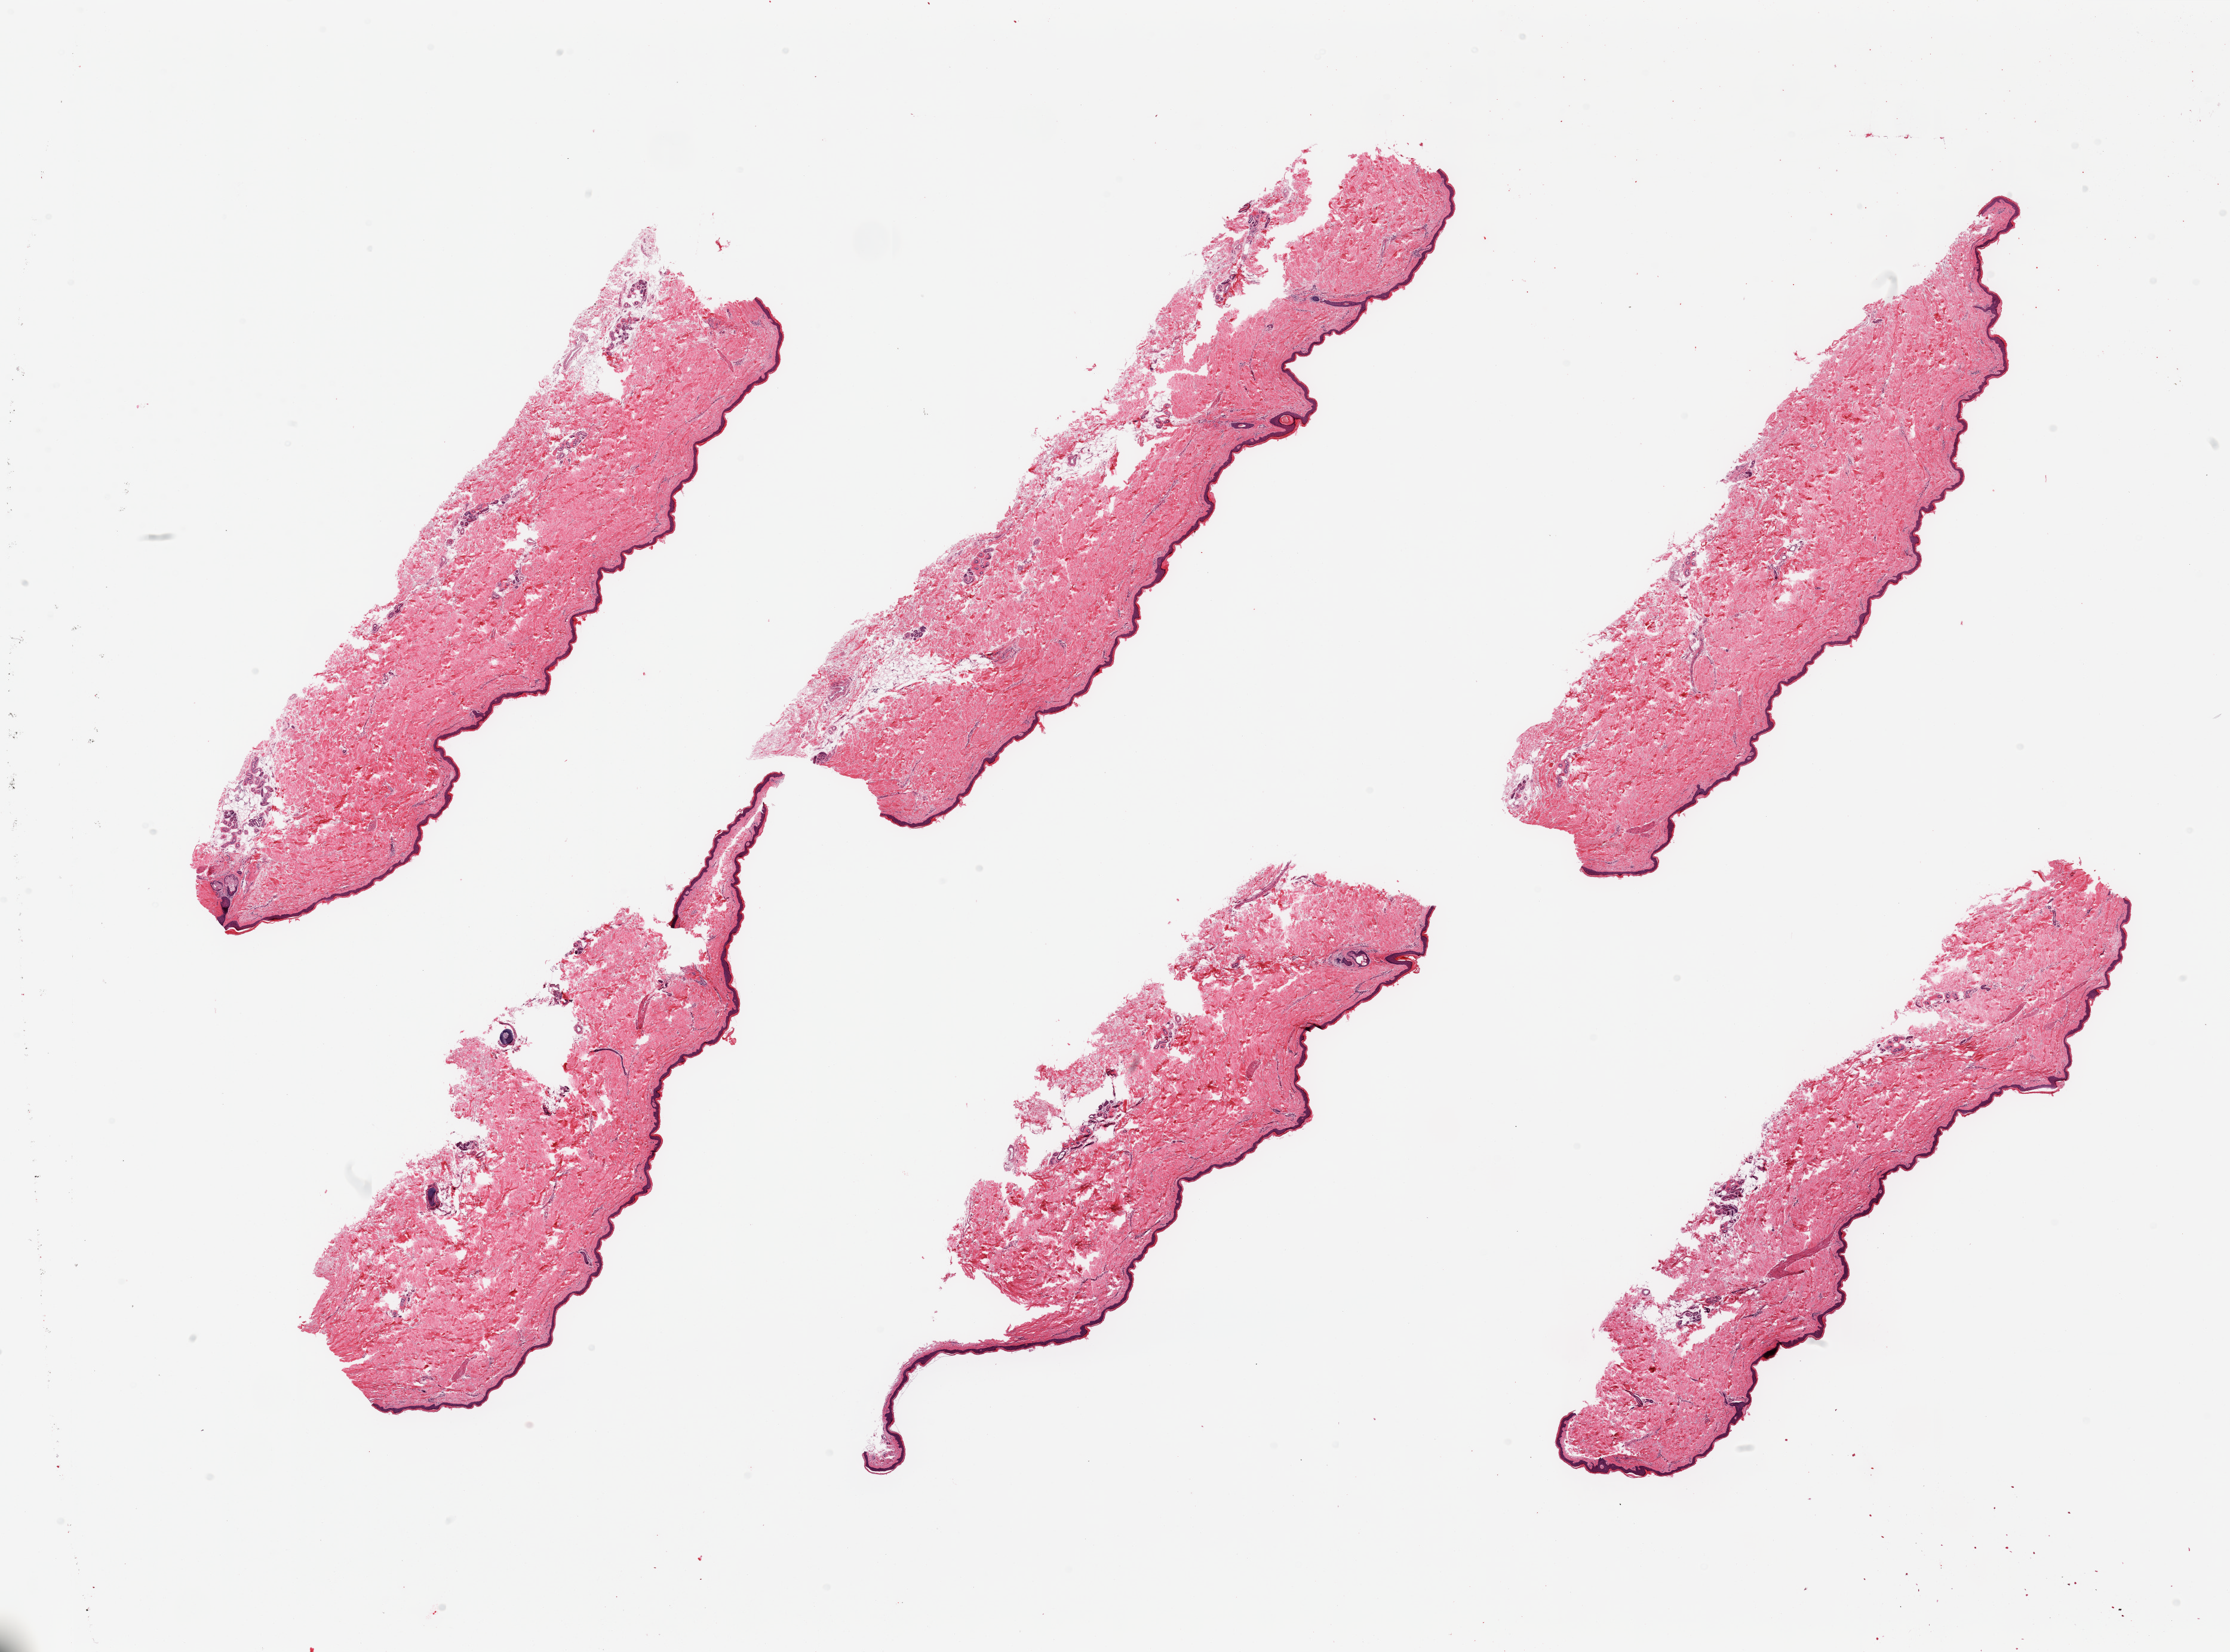
Hematoxylin and eosin (H&E) whole-slide image, brightfield, a low-resolution overview of the entire scanned area, about 29.5 x 21.9 mm, PAXgene-fixed paraffin-embedded (PFPE) section, section of skin of lower leg (target tissue), tissue donor sample.
• pathologist's review note for this sample: 6 pieces, no adherent fat; squamous epithelium is ~30-40 microns